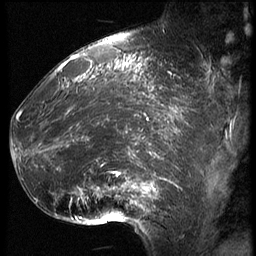
Breast MRI (dynamic contrast-enhanced), one sagittal slice. Slice 22 of 62 in the series (ordered by position). 3 images stored at this slice position (order not interpretable as contrast timing). 1.5 T. TE 4.2 ms, TR 9 ms. 2.5 mm slice thickness. 256 × 256 image matrix, field of view 180 × 180 mm. Patient: female, 39 years. From the clinical record (not read from this slice): setting: breast cancer imaged before/during neoadjuvant chemotherapy; receptor status: HER2-positive.
Outlined on this slice (semi-automatic segmentation, software-assisted and operator-edited):
- analysis volume of interest (the breast-tissue region the enhancement analysis was run in; not a lesion): bounding box <16,64,171,228> (left, top, right, bottom; pixels)
- tumour enhancement mask (voxels above the 140 % enhancement threshold inside the analysis volume of interest): <16,64,171,224>